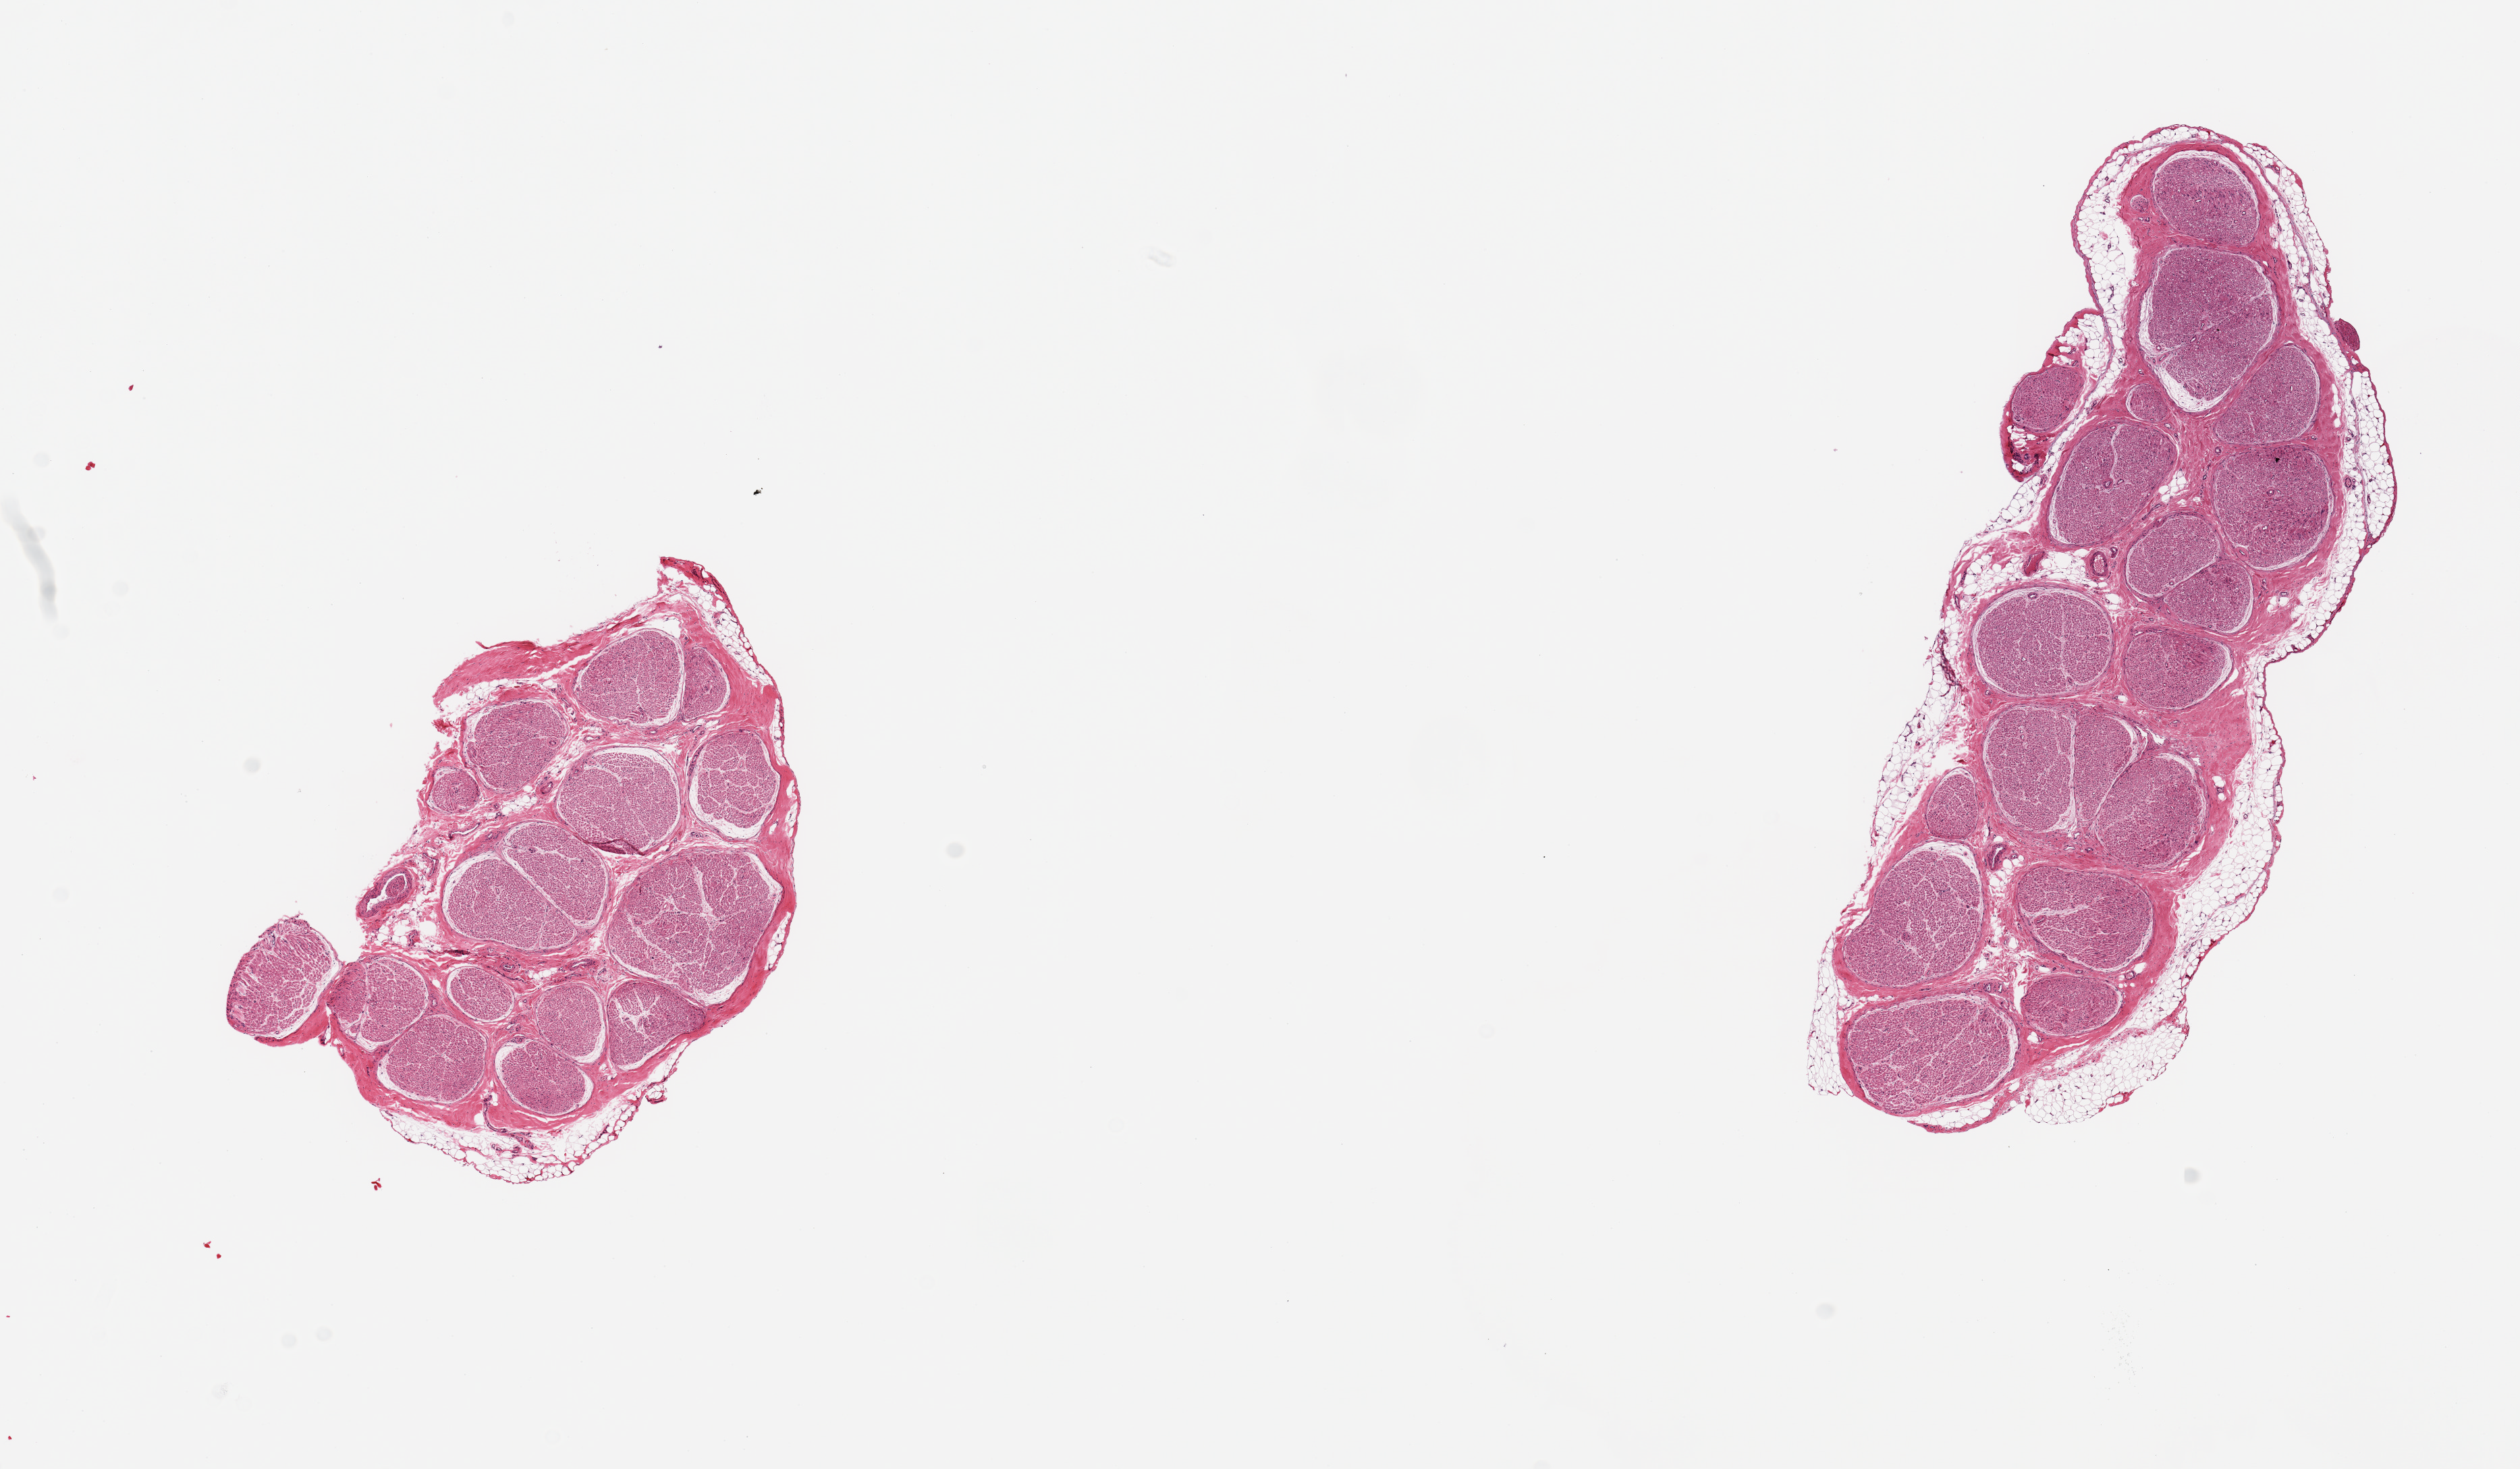
Haematoxylin and eosin whole-slide image, low-resolution overview of the scanned area, about 14.8 x 8.6 mm; PAXgene-fixed paraffin-embedded (PFPE) section; target tissue: tibial nerve; tissue donor sample. Female donor.
Pathologist's review note for this sample: 2 pieces; thin (0.3 mm) rim of fat coats external aspect.